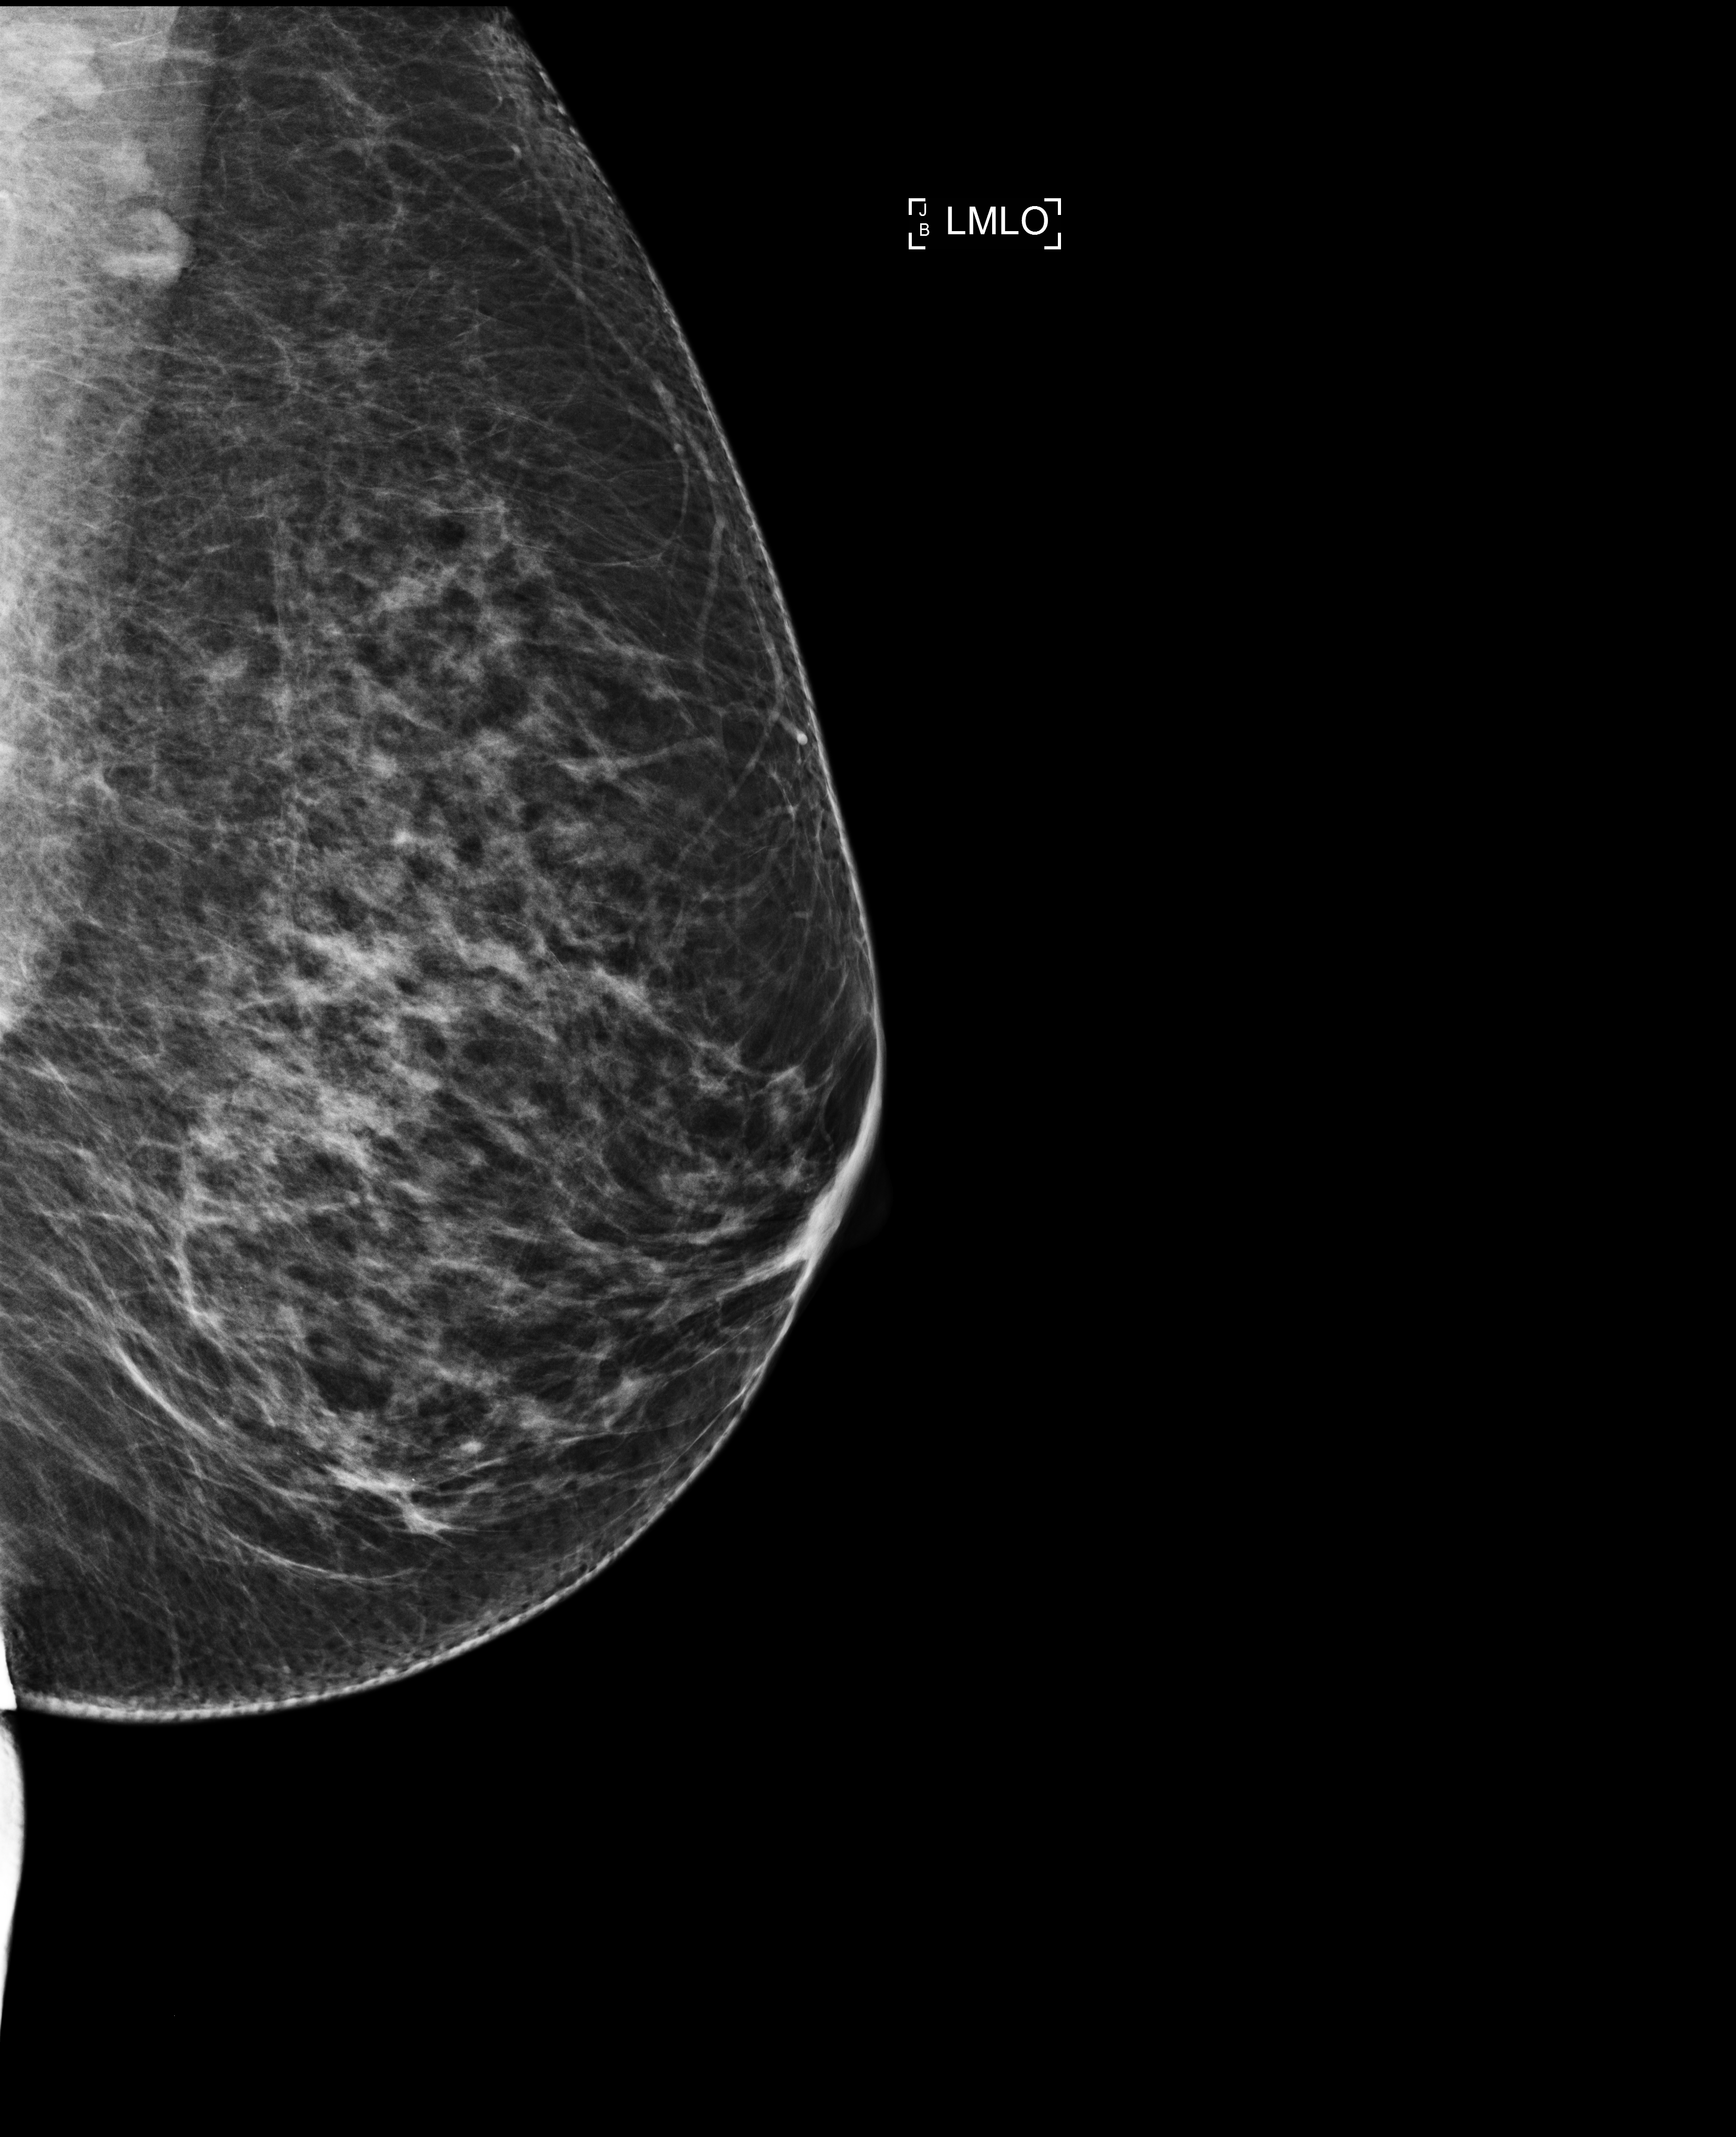
Full-field digital mammogram (FFDM), left breast, MLO view, screening examination, compressed breast thickness 73 mm. Patient: female, 62 years.
Final BI-RADS assessment for this screening round (tomosynthesis exam, both breasts): category 2.